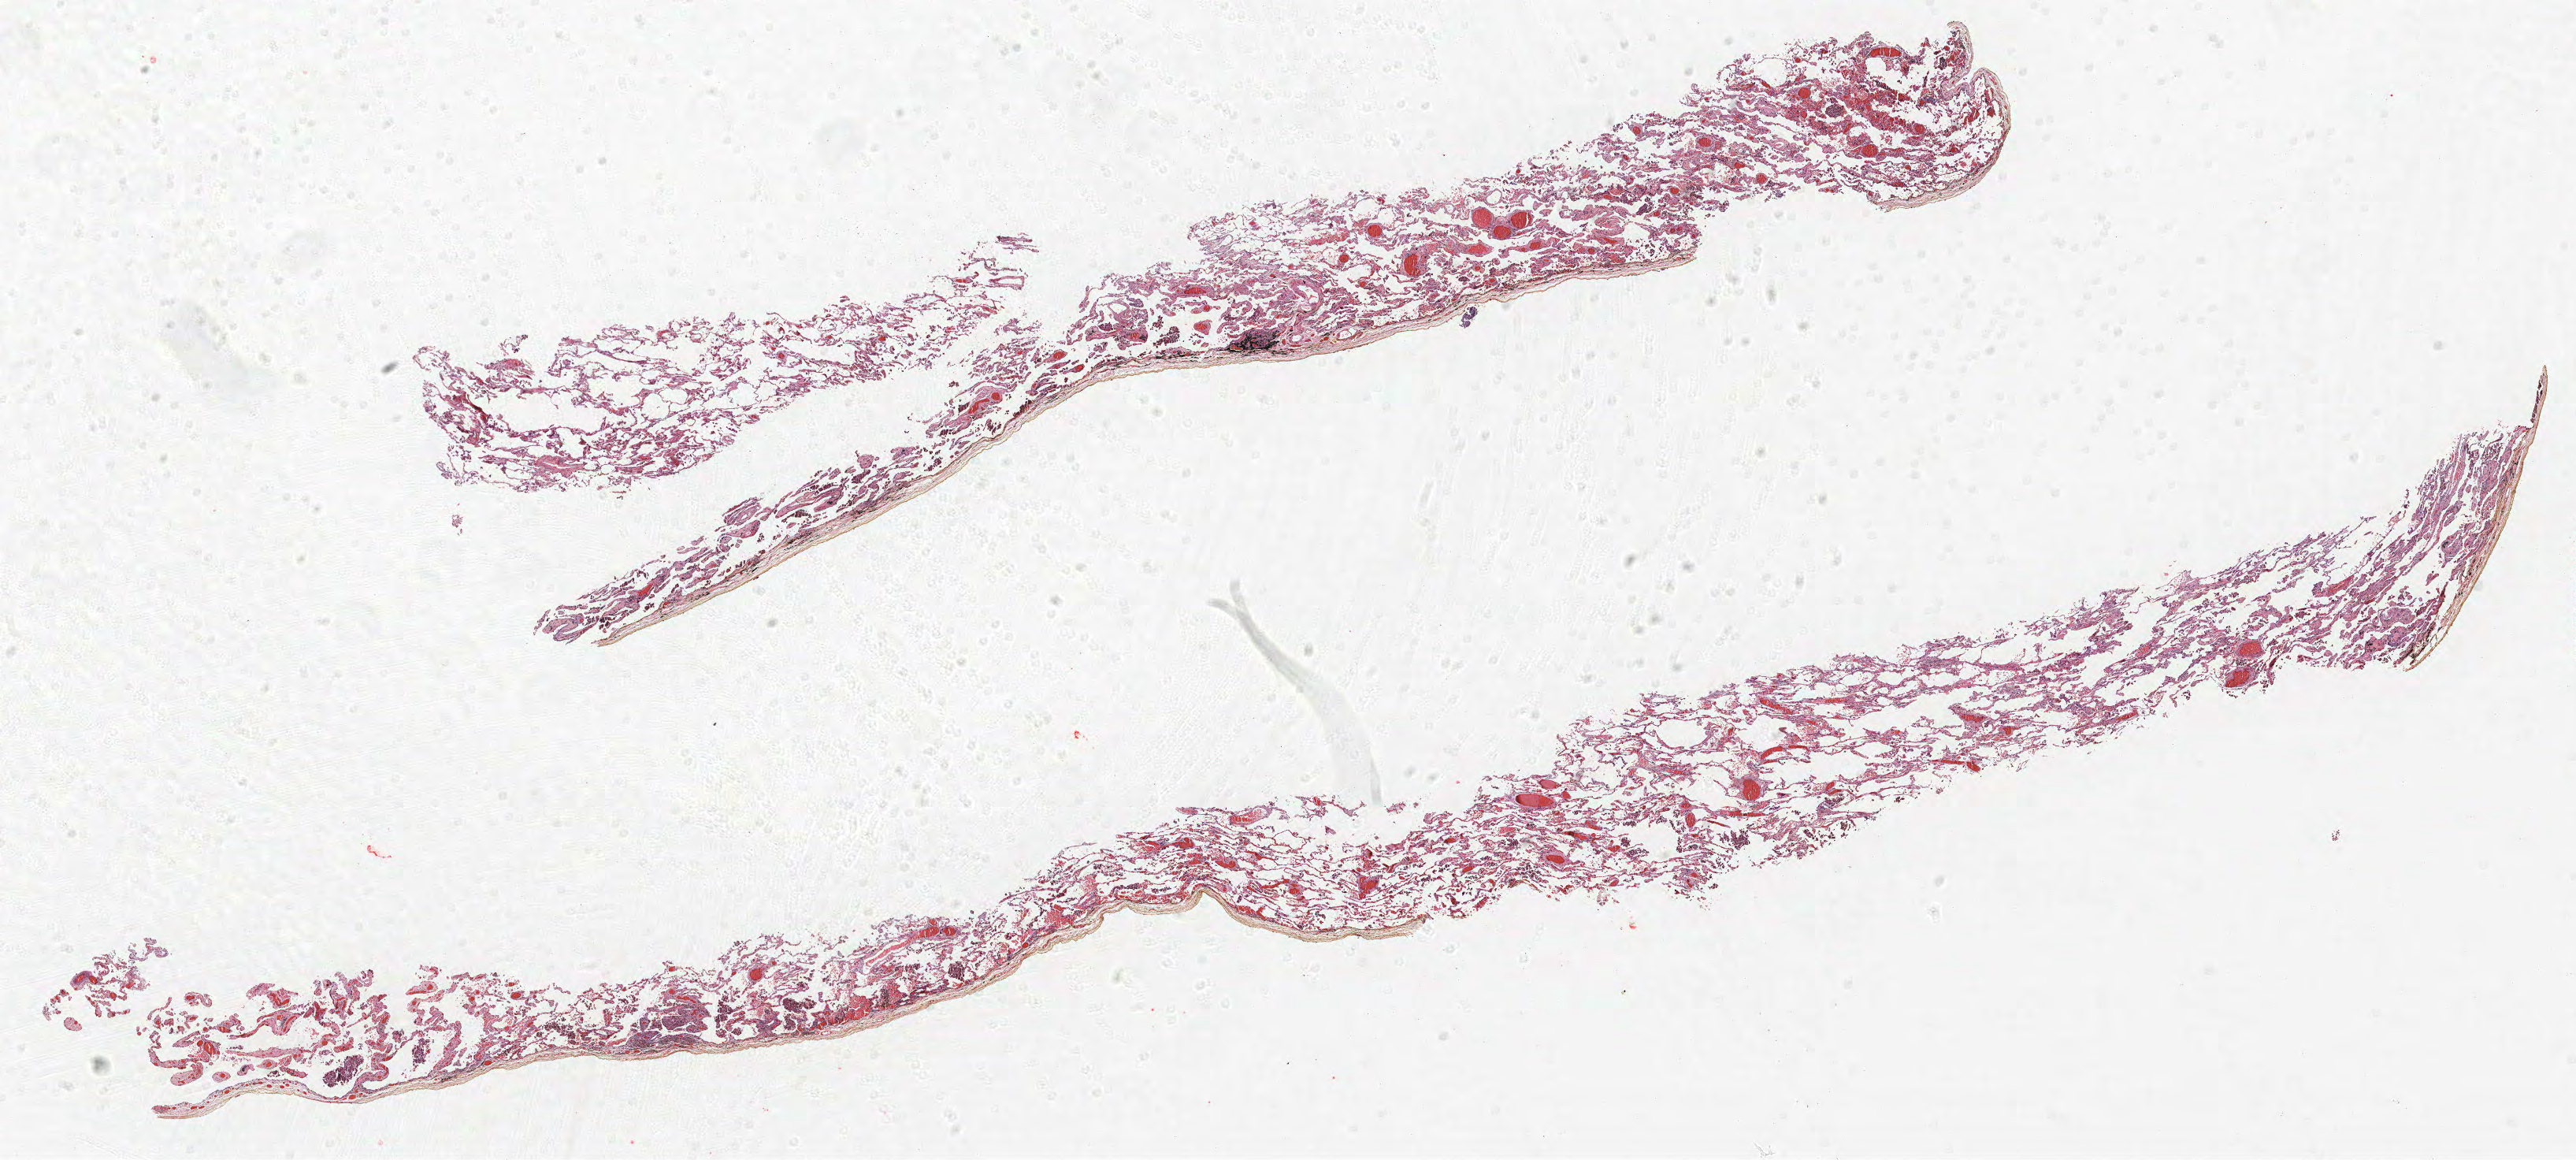
Whole-slide histology image, H&E — shown as a low-resolution overview of the whole scanned area (about 26.2 x 11.8 mm); FFPE section; lung. Male patient, aged 63 at enrolment. Current smoker at enrolment. Grade: moderately differentiated (G2).
Stage (AJCC 6th edition): IA. Primary tumour location (clinical record): right lower lobe. ICD-O-3 topography: lower lobe of lung (C34.3). Tumour size (pathology): 12 mm. Participant's lung-cancer diagnosis: Adenocarcinoma, NOS (ICD-O-3 8140/3). Note: participant had 3 primary lung cancers recorded; fields above describe the first.